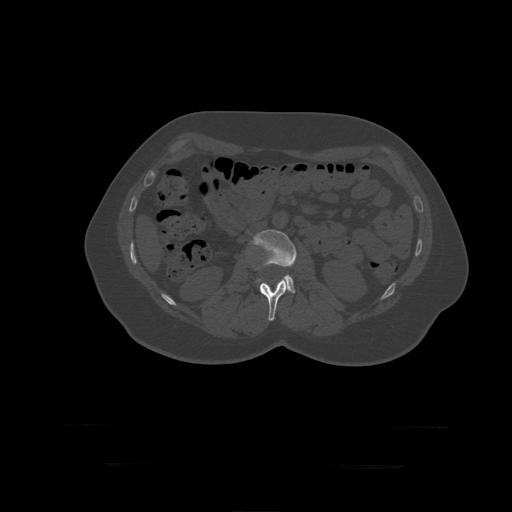
CT including the spine, one axial slice; position 138 of 399 along the scan axis; reconstruction kernel STANDARD; 120 kVp; bone window (W 1800 / L 400 HU); 512 × 512 image matrix, field of view 450 × 450 mm. Patient age 41 years. Case-level facts recorded for this patient, not image findings: primary cancer: breast.
Outlined on this slice (semi-automatic segmentation, software-assisted and operator-edited):
- L2 vertebra: bounding box <260,280,288,321> (left, top, right, bottom; pixels)
- L3 vertebra: <251,230,297,294>